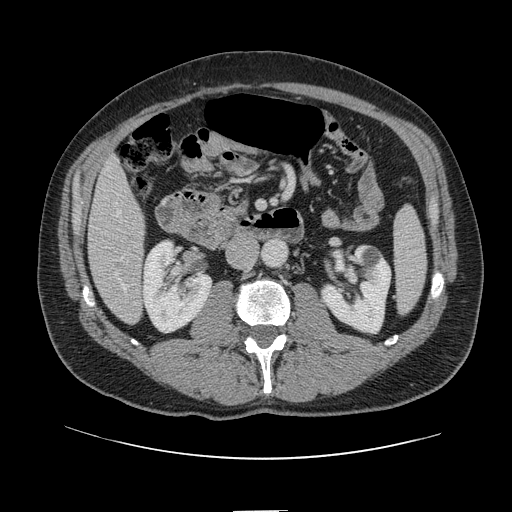
Contrast-enhanced abdominal CT, one axial slice. Position 33 of 161 along the scan axis. 120 kVp. Intravenous contrast given. Soft-tissue window (W 400 / L 40 HU). 2.5 mm slice thickness. 512 × 512 image matrix, field of view 412 × 412 mm. Male patient, age 66 years. Case-level facts recorded for this patient, not image findings: diagnosis: colorectal cancer liver metastases, imaged before liver resection; multiple liver metastases: no; largest metastasis: 3.5 cm.
Annotated regions visible in this slice (manually delineated by an expert):
- hepatic veins: bounding box (x1, y1, x2, y2) in pixels: (116, 212, 127, 290)
- liver: (89, 160, 145, 323)
- planned liver remnant (the part of the liver to remain after resection): (88, 160, 144, 263)